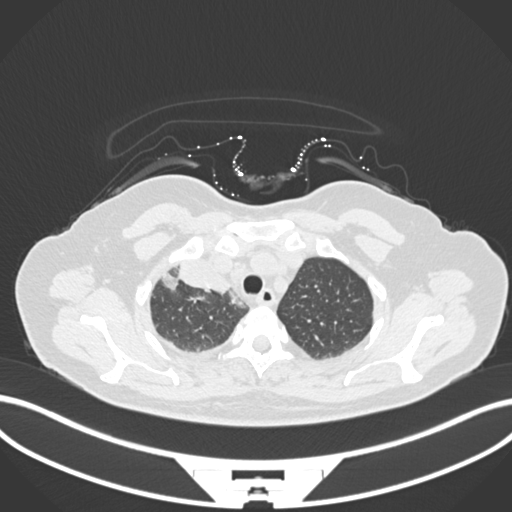
Chest CT, one axial slice; slice 139 of 172 in the series (ordered by position); reconstruction kernel B30f; 120 kVp; lung window (W 1500 / L -600 HU); 1 mm slice thickness; 512 × 512 image matrix, field of view 400 × 400 mm. Patient: female, 52 years. Case-level facts recorded for this patient, not image findings: clinical TNM (as recorded): T3 N1 M1.
Outlined on this slice (rectangle marked by the reading radiologist):
- lung tumour (recorded histology: adenocarcinoma): bounding box <157,259,235,296> (left, top, right, bottom; pixels)